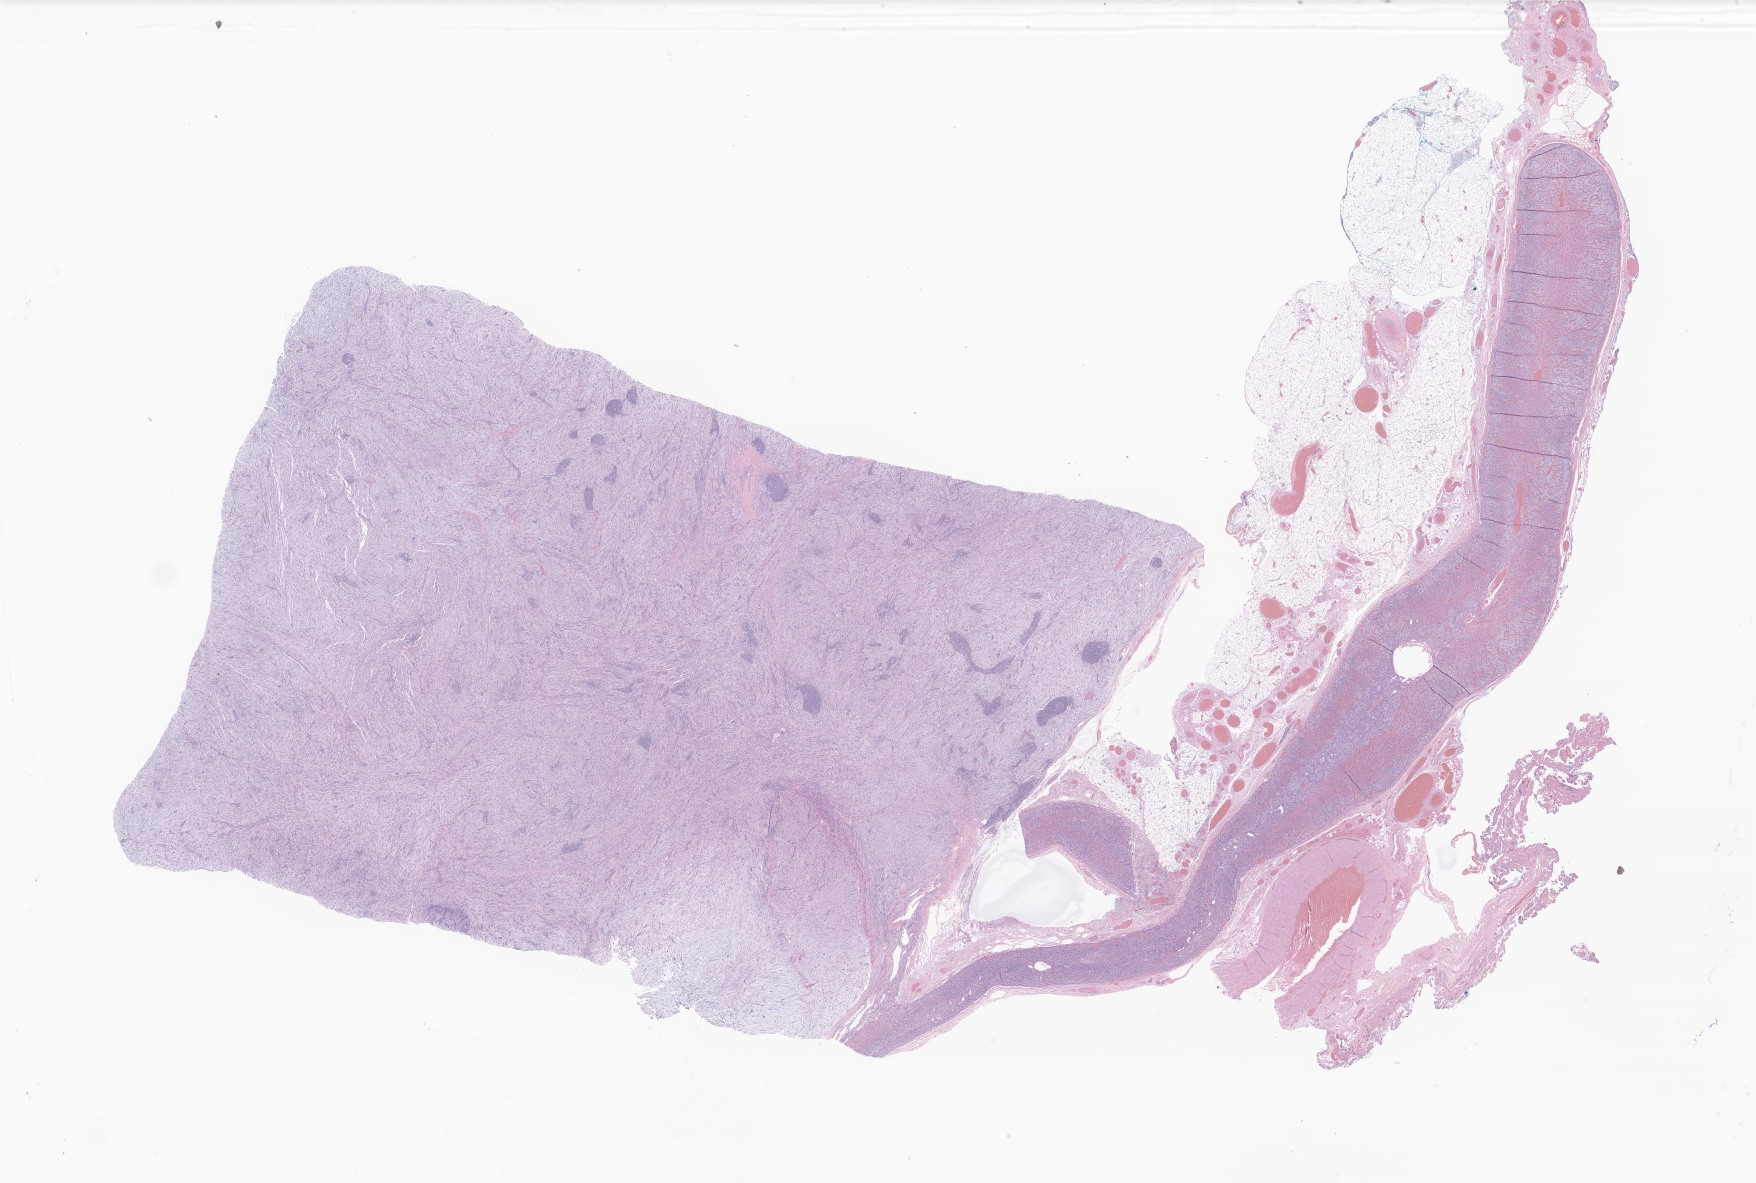
Whole-slide image, hematoxylin and eosin (H&E) stain of tumor tissue from the abdomen — low-resolution overview of the scanned area, about 29.6 x 20.0 mm, formalin-fixed, paraffin-embedded (FFPE) tissue. Patient: female, age 60 months (5 years).
Recorded diagnosis: Myofibroblastic tumor, NOS.